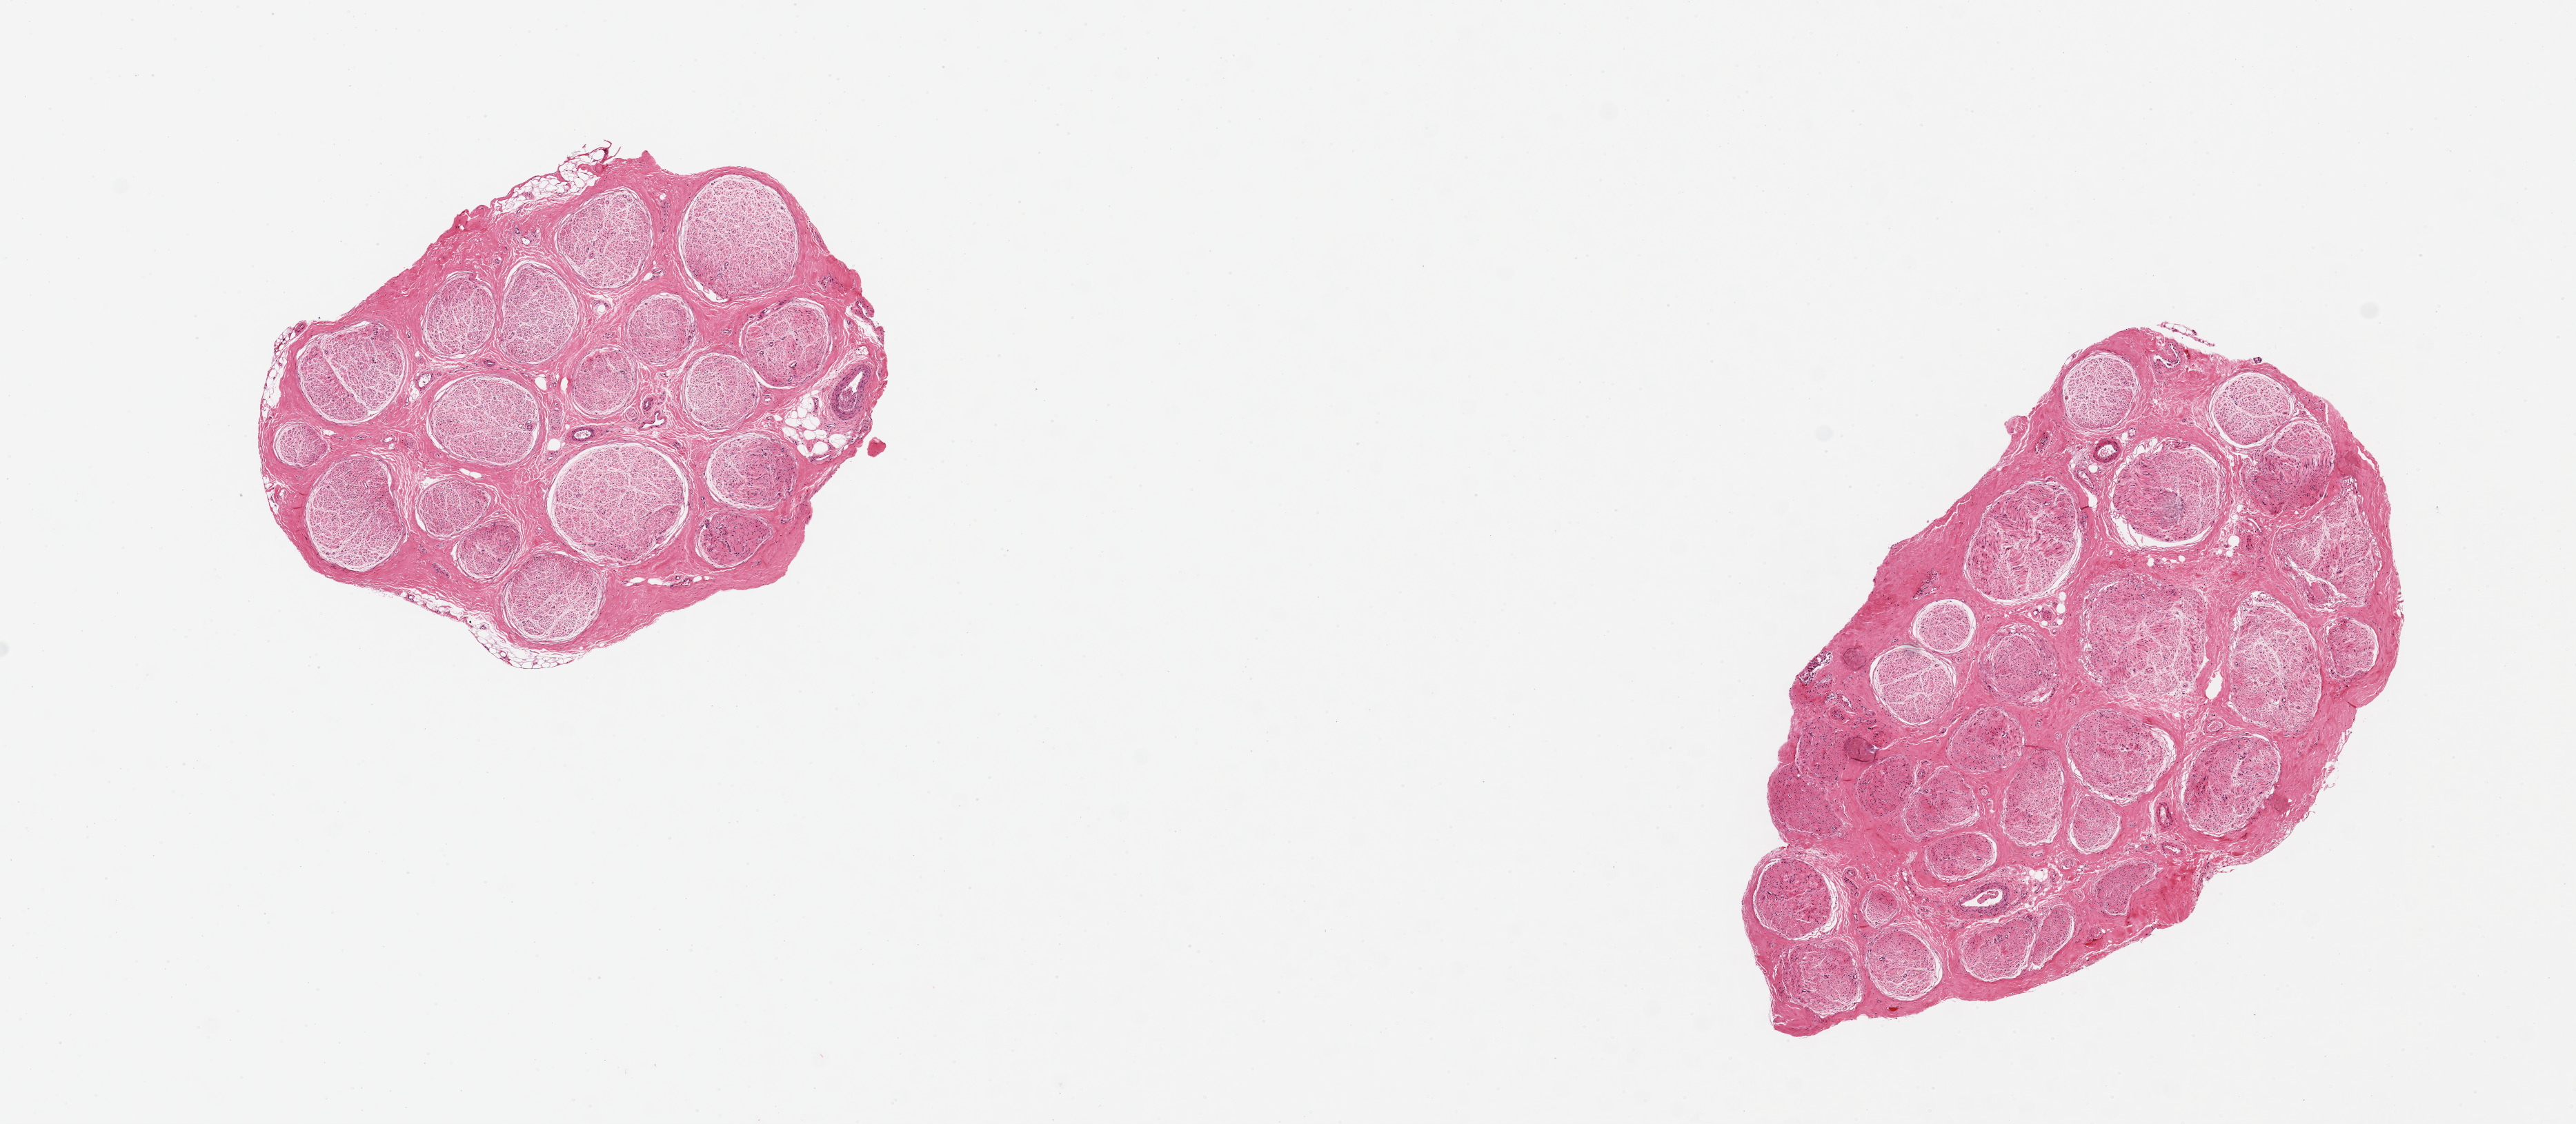
Whole-slide image, H&E stain — a low-resolution overview of the entire scanned area, about 14.8 x 6.4 mm (from a 20x scan). PAXgene-fixed paraffin-embedded (PFPE) section. Target tissue: tibial nerve. Donor tissue sample. Male donor.
- pathologist's review note for this sample: 2 pieces ~4.5mm d. Good clean specimens, minimal fat